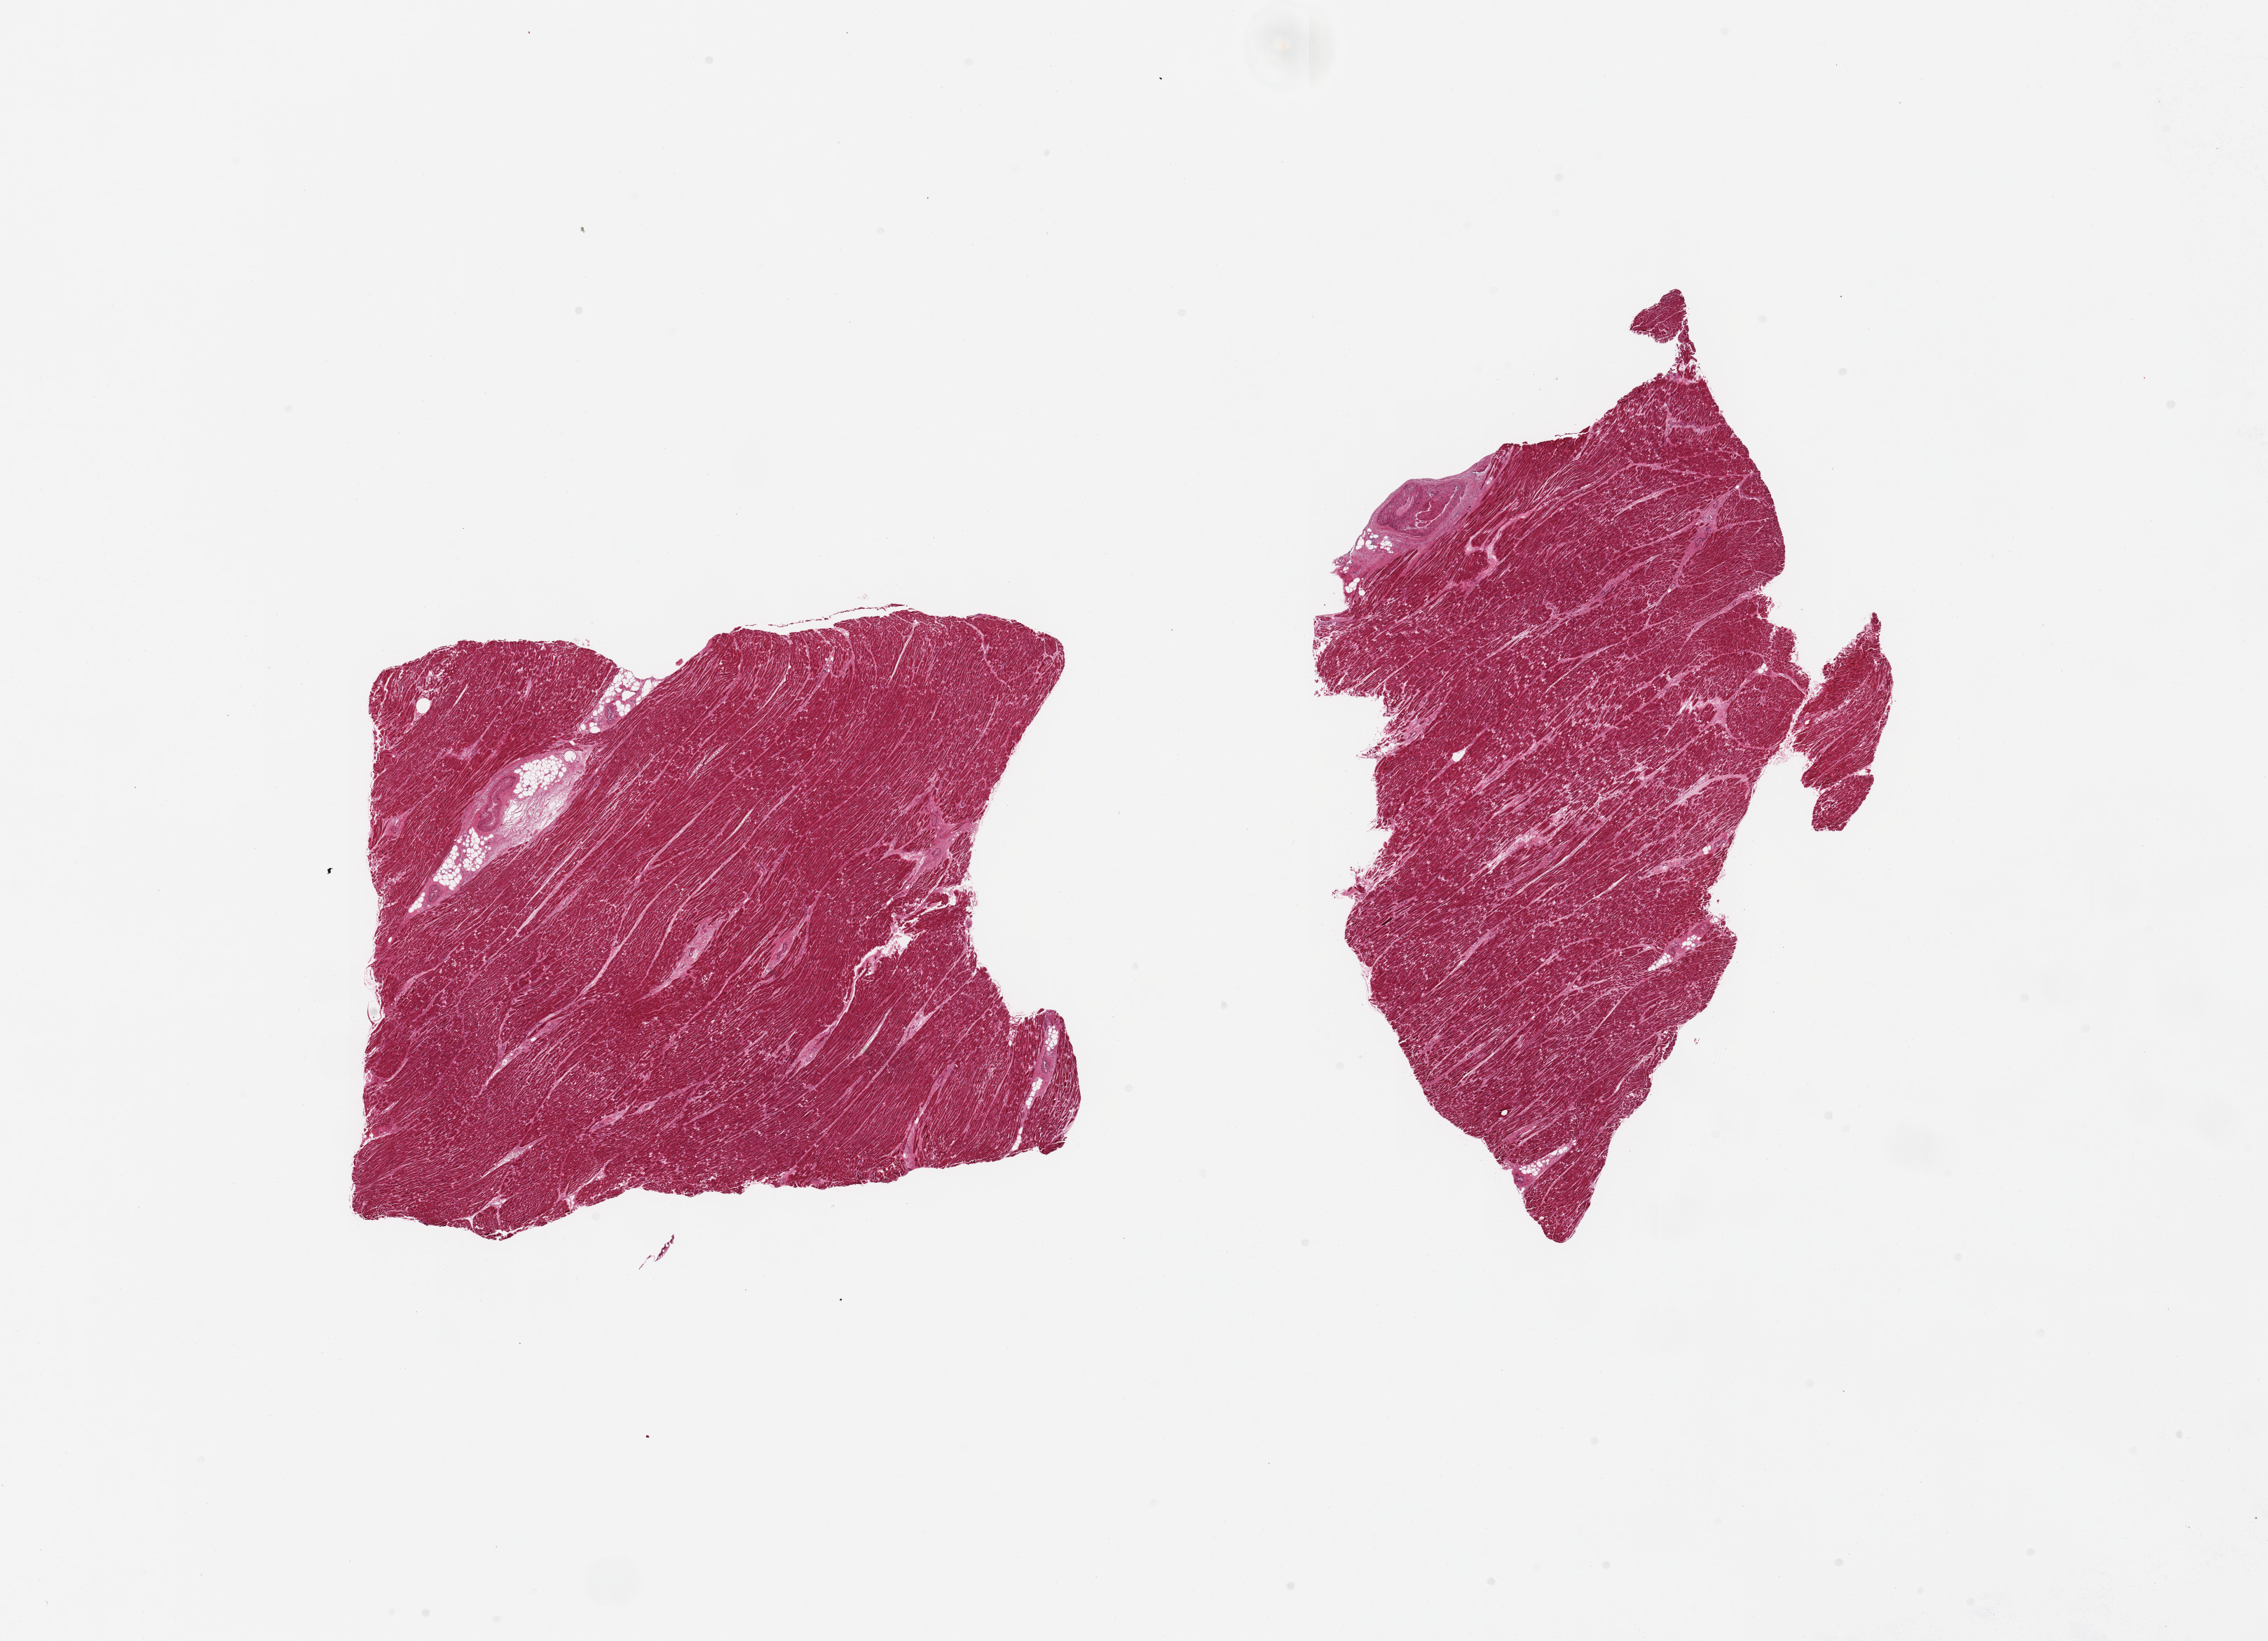
Haematoxylin and eosin whole-slide image, whole scanned area (about 25.6 x 18.5 mm, acquisition: 20x scan) shown as a low-resolution overview. PAXgene-fixed paraffin-embedded (PFPE) section. Sampled site (target tissue): heart. Tissue donor sample. Male donor.
Review note (as recorded): 2 pieces, mild interstitial fibrosis/ ischemic change.